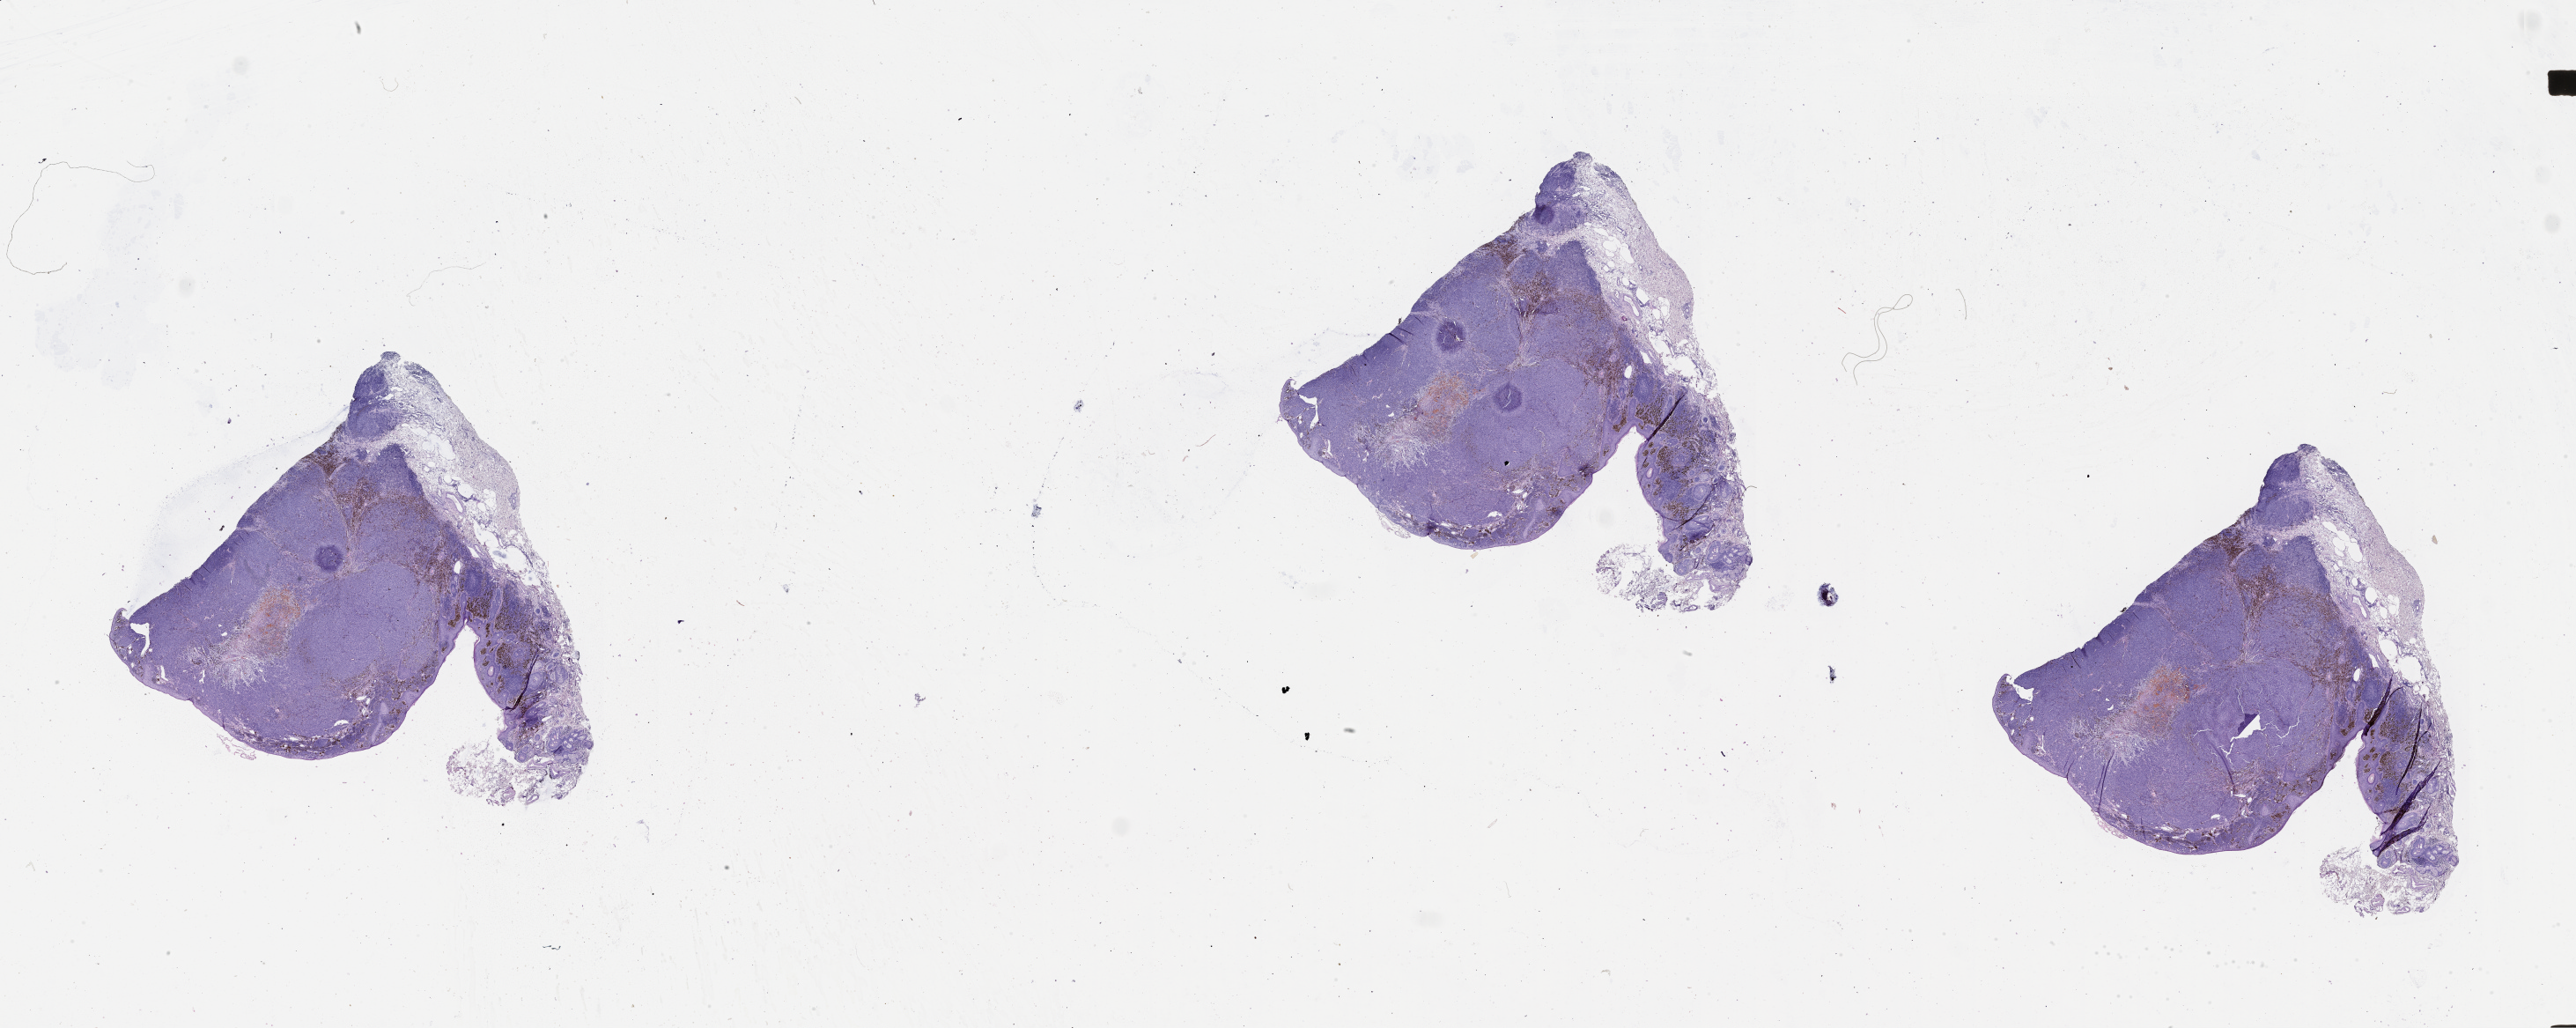
Digitized H&E tissue section (whole slide) — low-resolution overview of the scanned area, about 47.1 x 18.8 mm; melanoma tumour tissue; sampled site not recorded. 83-year-old male patient.
• AJCC pathologic stage: IIC
• histologic diagnosis: Malignant melanoma, NOS
• primary tumour site (as recorded): head & neck